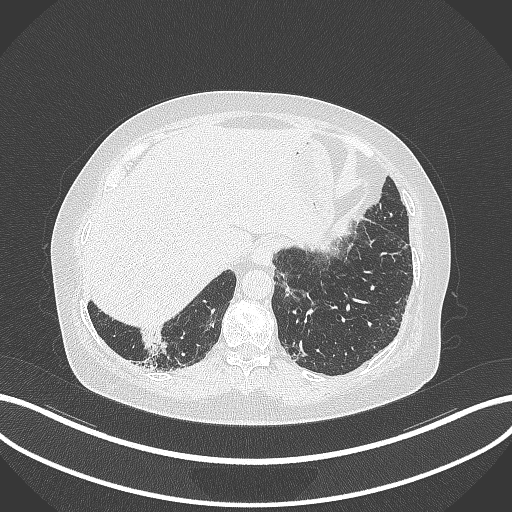
Chest CT, one axial slice; lung window (W 1500 / L -600 HU); 512 × 512 image matrix. Patient: female, 65 years. Case-level facts recorded for this patient, not image findings: clinical TNM (as recorded): T2b N1 M0; histopathological grade: G1.
Annotated regions visible in this slice (bounding box drawn by a radiologist):
- lung tumour (recorded histology: adenocarcinoma): box from (x=137, y=326) to (x=167, y=357) px